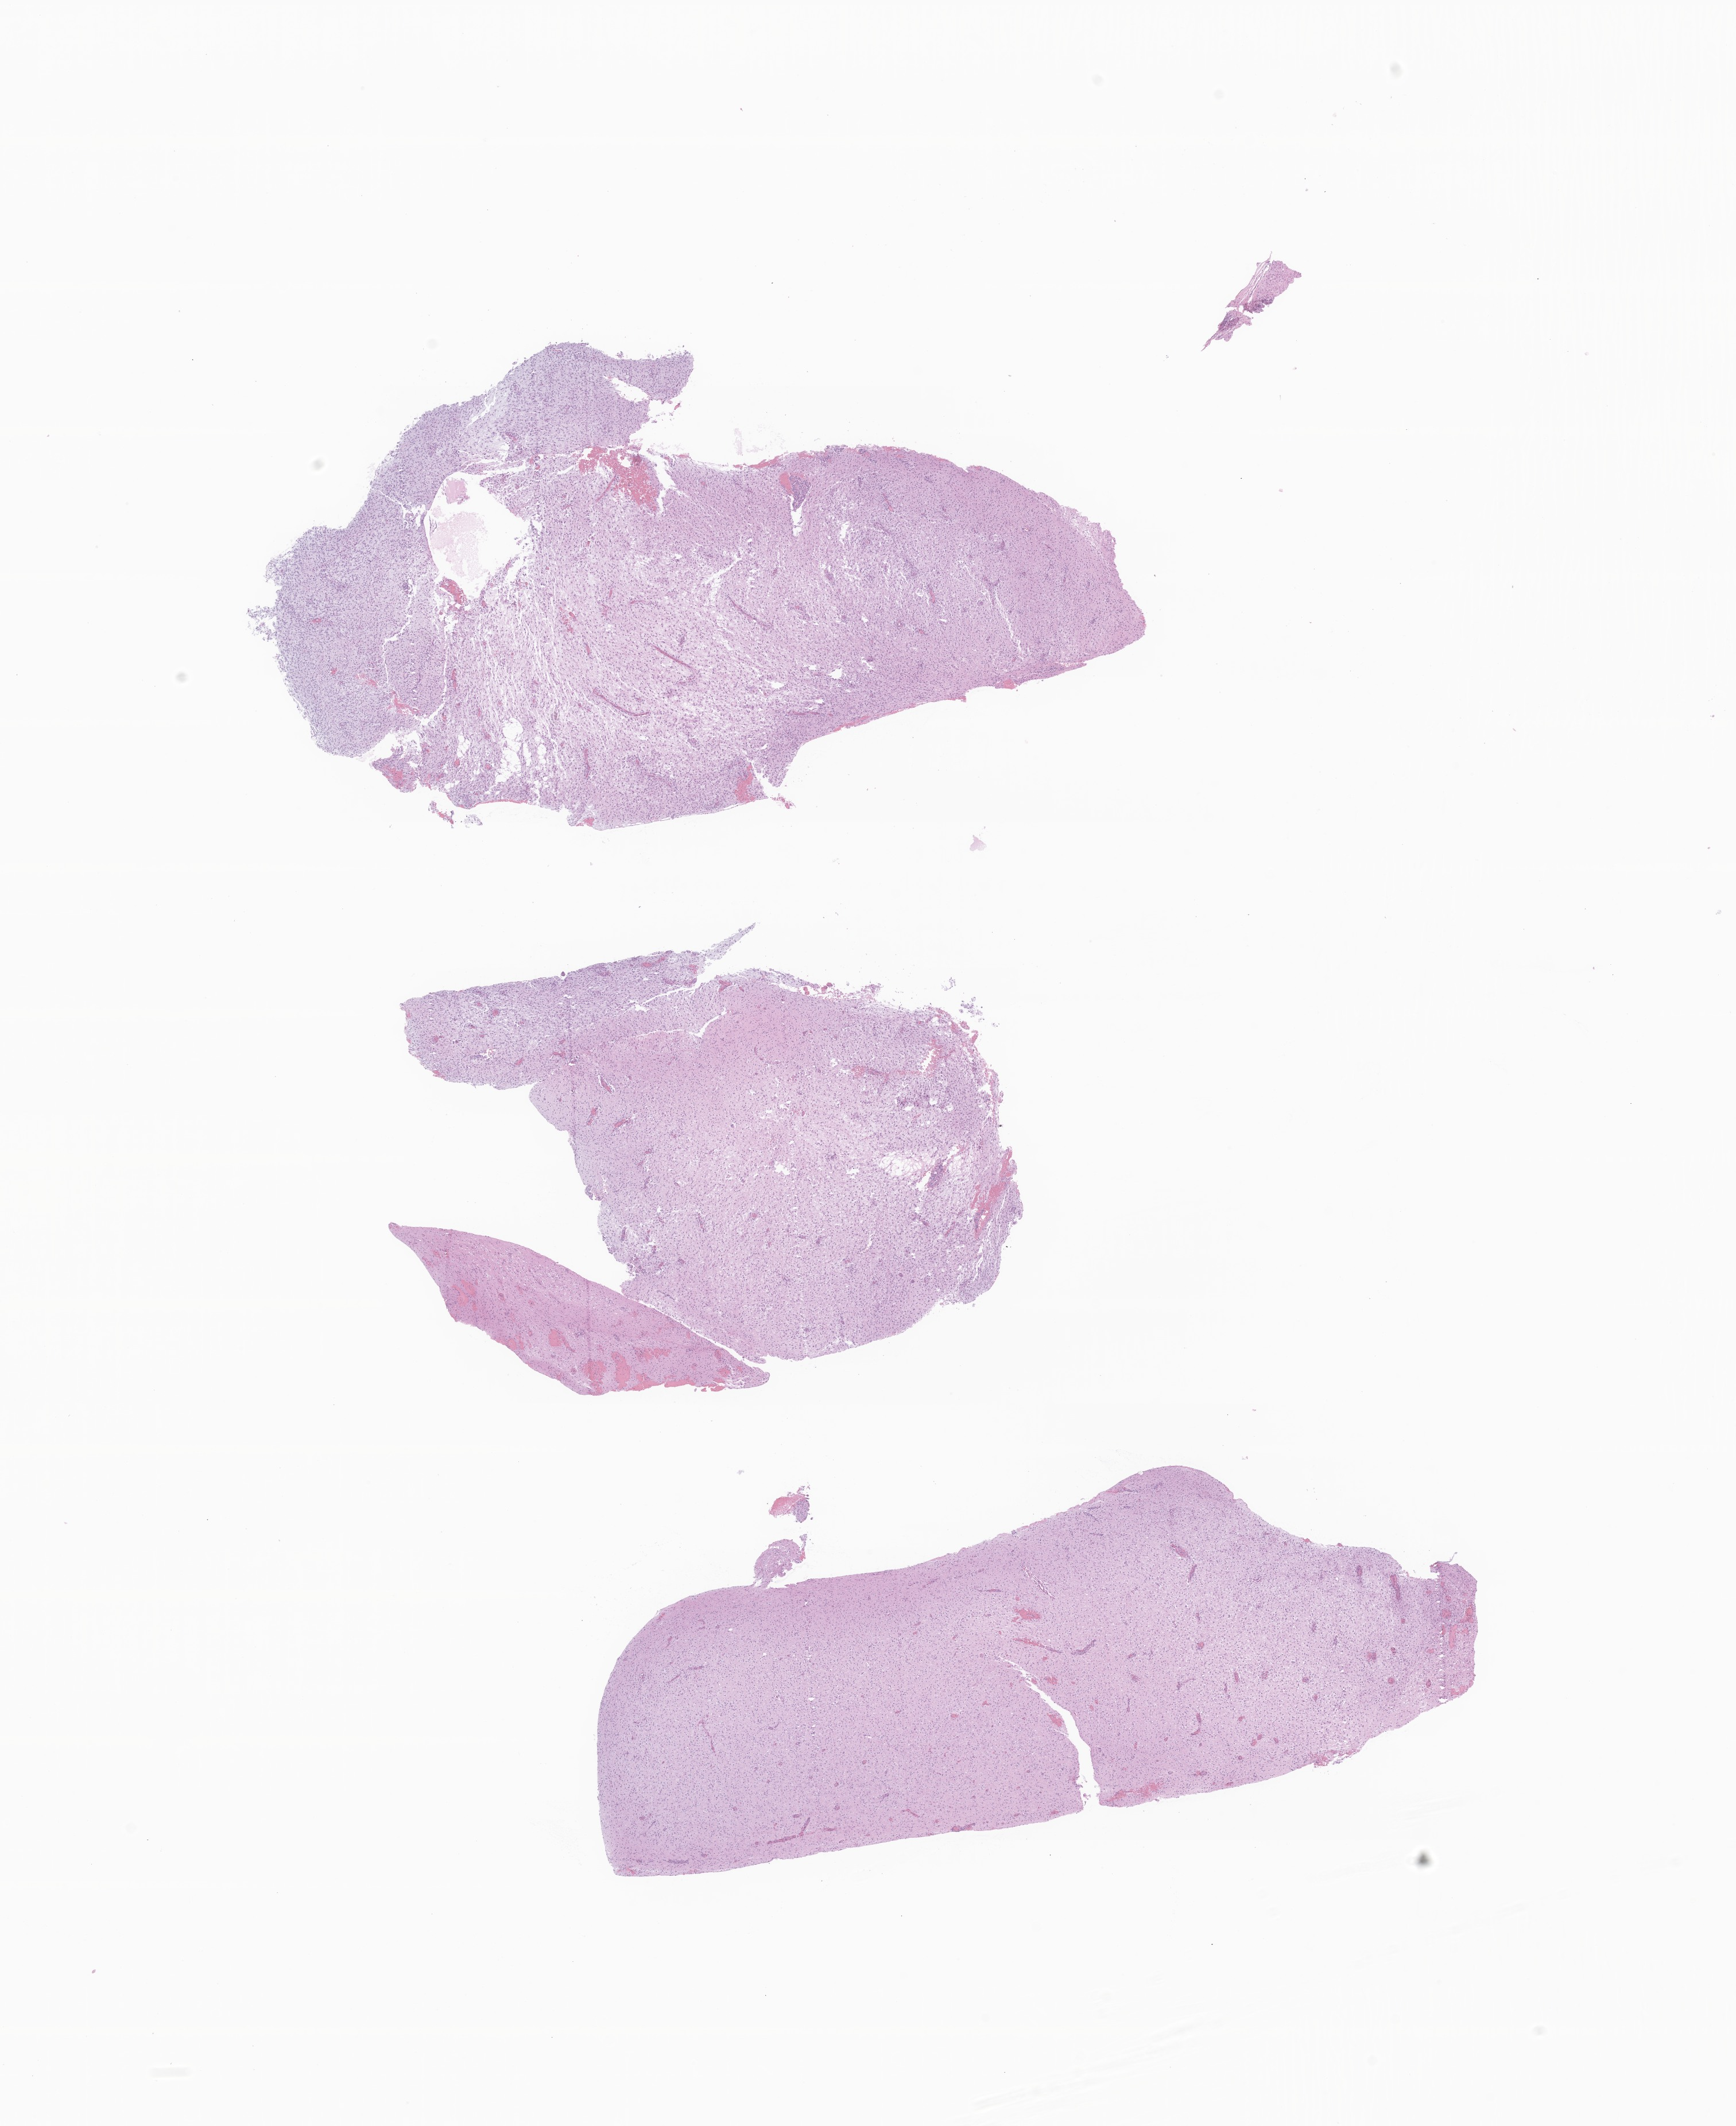
Digitized hematoxylin and eosin (H&E)-stained section of tumor tissue from the brain — low-resolution overview of the scanned area, about 12.7 x 15.6 mm, formalin-fixed paraffin-embedded section. Patient male; age 287 days.
Recorded diagnosis: Neoplasm, uncertain whether benign or malignant.